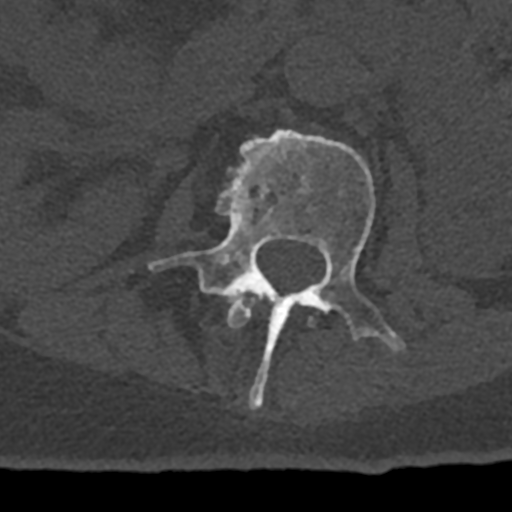
CT including the spine, one axial slice; slice 386 of 797 in the series (ordered by position); 120 kVp; bone window (W 1800 / L 400 HU); 0.5 mm slice thickness; 512 × 512 image matrix, field of view 160 × 160 mm. Patient: male, 74 years. Case-level facts recorded for this patient, not image findings: primary cancer: renal; vertebrae with lytic lesions (as recorded): T10, L1, L2, L3, L4, L5.
Annotated regions visible in this slice (semi-automatically segmented with operator editing):
- L1 vertebra: bounding box <227,291,313,328> (left, top, right, bottom; pixels)
- L2 vertebra: <149,129,405,410>